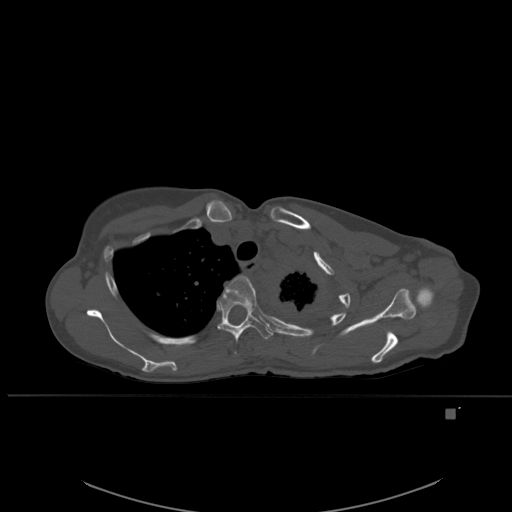
CT including the spine, one axial slice. Position 416 of 537 along the scan axis. Bone window (W 1800 / L 400 HU). 512 × 512 image matrix. Patient: female, 45 years. Case-level facts recorded for this patient, not image findings: primary cancer: lung.
Outlined on this slice (semi-automatically segmented with operator editing):
- T3 vertebra: box from (x=225, y=276) to (x=257, y=353) px
- T4 vertebra: (x=217, y=292)–(x=273, y=344)